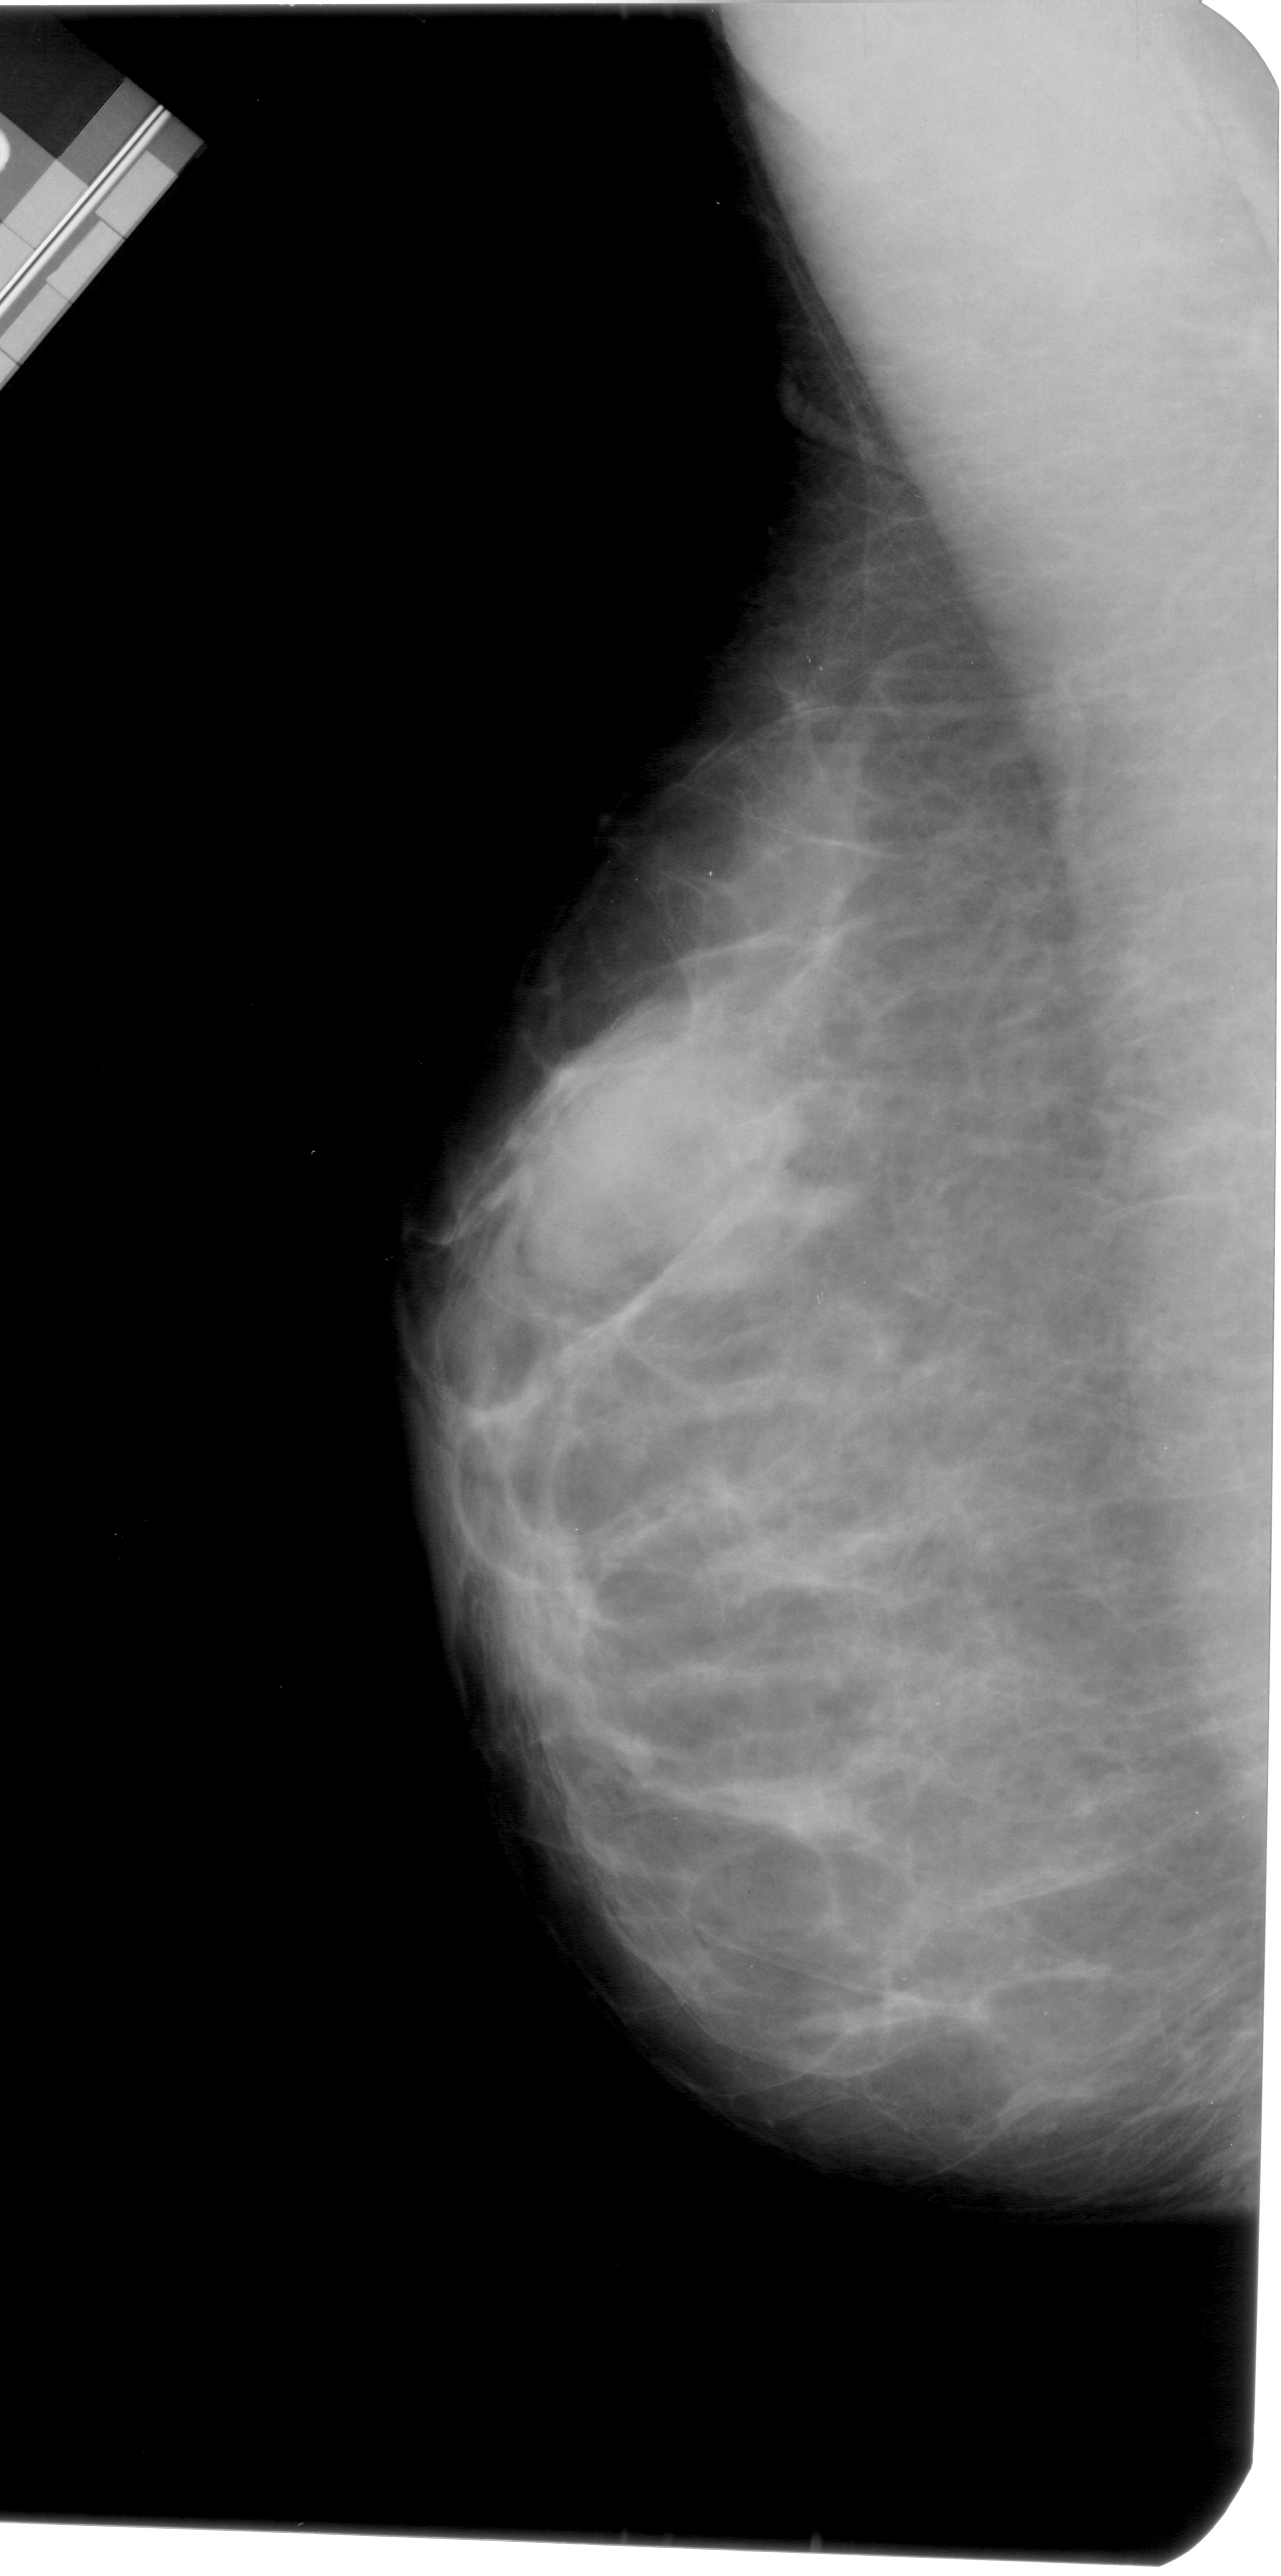
Digitized screen-film mammogram; left breast; MLO view; breast composition: extremely dense (BI-RADS density category 4 of 4).
Mass, shape oval, margins obscured; BI-RADS assessment category 4; pathology result (as recorded, not read from the image): benign.